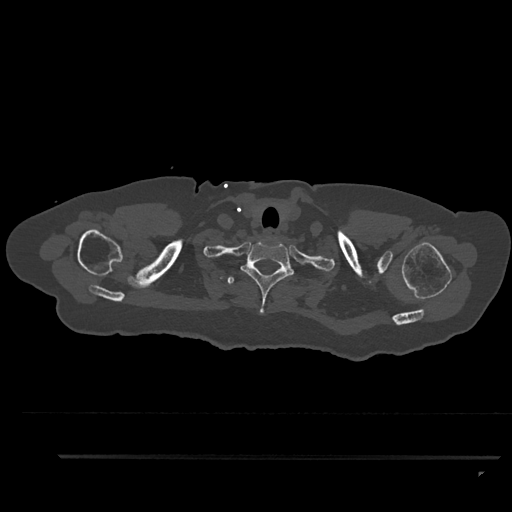
CT including the spine, one axial slice; slice 760 of 797 in the series (ordered by position); reconstruction kernel Br40s/3; bone window (W 1800 / L 400 HU); 0.5 mm slice thickness; 512 × 512 image matrix, field of view 408 × 408 mm. Patient: female, 44 years. Case-level facts recorded for this patient, not image findings: primary cancer: renal.
Structures marked on this image (semi-automatic segmentation, software-assisted and operator-edited):
- T1 vertebra: bounding box (x1, y1, x2, y2) in pixels: (240, 241, 295, 313)
- T2 vertebra: (227, 277, 234, 284)